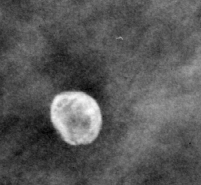
Crop from a digitized film mammogram around one marked abnormality; right breast; MLO view; BI-RADS breast density category 3 (scale 1–4).
Marked abnormality: calcifications, morphology round and regular / eggshell; BI-RADS assessment category 2; subtlety rating 3 on a 1 (subtle) to 5 (obvious) scale; benign; no additional work-up was recommended (benign without callback).